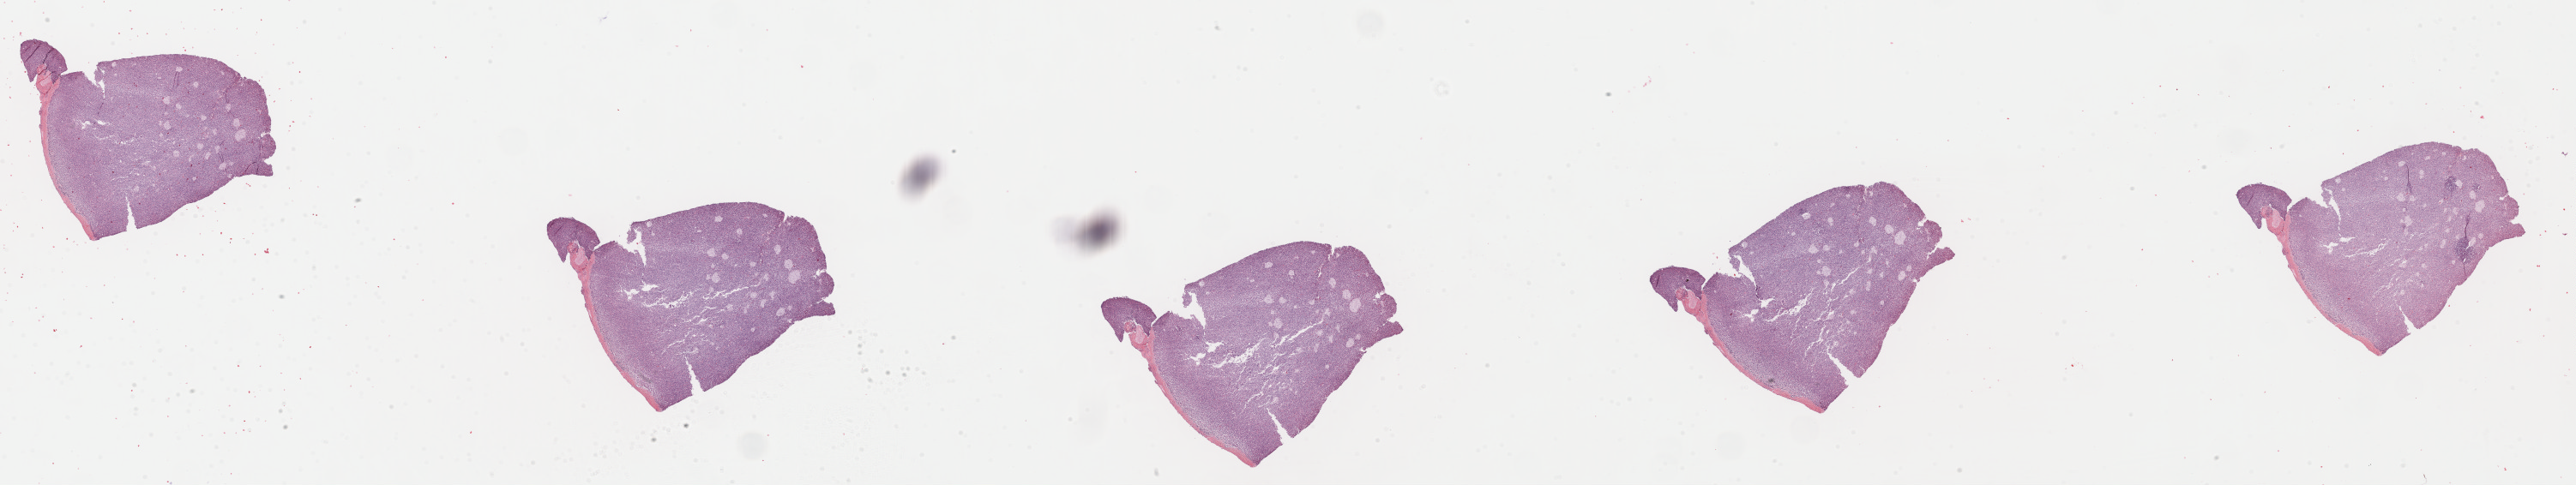
Digitized Hematoxylin and eosin (H&E) stained tissue section (whole slide) — whole scanned area (about 47.4 x 8.9 mm, from a 40x scan) shown as a low-resolution overview, formalin-fixed paraffin-embedded (FFPE) diagnostic section, kidney, primary tumour sample. Patient: female, age at initial diagnosis 66 years. Slide review estimates, as recorded: tumour cells 75%, tumour nuclei 75%, normal cells 0%, stromal cells 25%, necrosis 0%. Inflammatory infiltration, as recorded: lymphocyte infiltration 2%, monocyte infiltration 6%, neutrophil infiltration 2%.
Pathologic diagnosis: Papillary adenocarcinoma, NOS. AJCC pathologic stage: I (7th edition). Laterality: left.